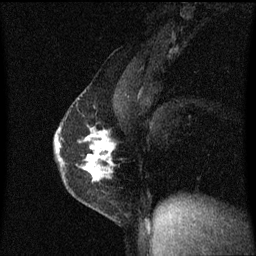
Breast MRI (dynamic contrast-enhanced), one sagittal slice; slice 37 of 60 in the series (ordered by position); dynamic contrast-enhanced series, image 2 of 3 at this slice position (ordered by acquisition); 1.5 T; TE 4.2 ms, TR 8.4 ms; 2 mm slice thickness; 256 × 256 image matrix, field of view 200 × 200 mm. Female patient, age 40 years.
Annotated regions visible in this slice (semi-automatically segmented with operator editing):
- analysis volume of interest (the breast-tissue region the enhancement analysis was run in; not a lesion): bounding box [x1, y1, x2, y2] px = [57, 112, 116, 191]
- tumour enhancement mask (voxels above the 70 % enhancement threshold inside the analysis volume of interest): [57, 128, 115, 181]